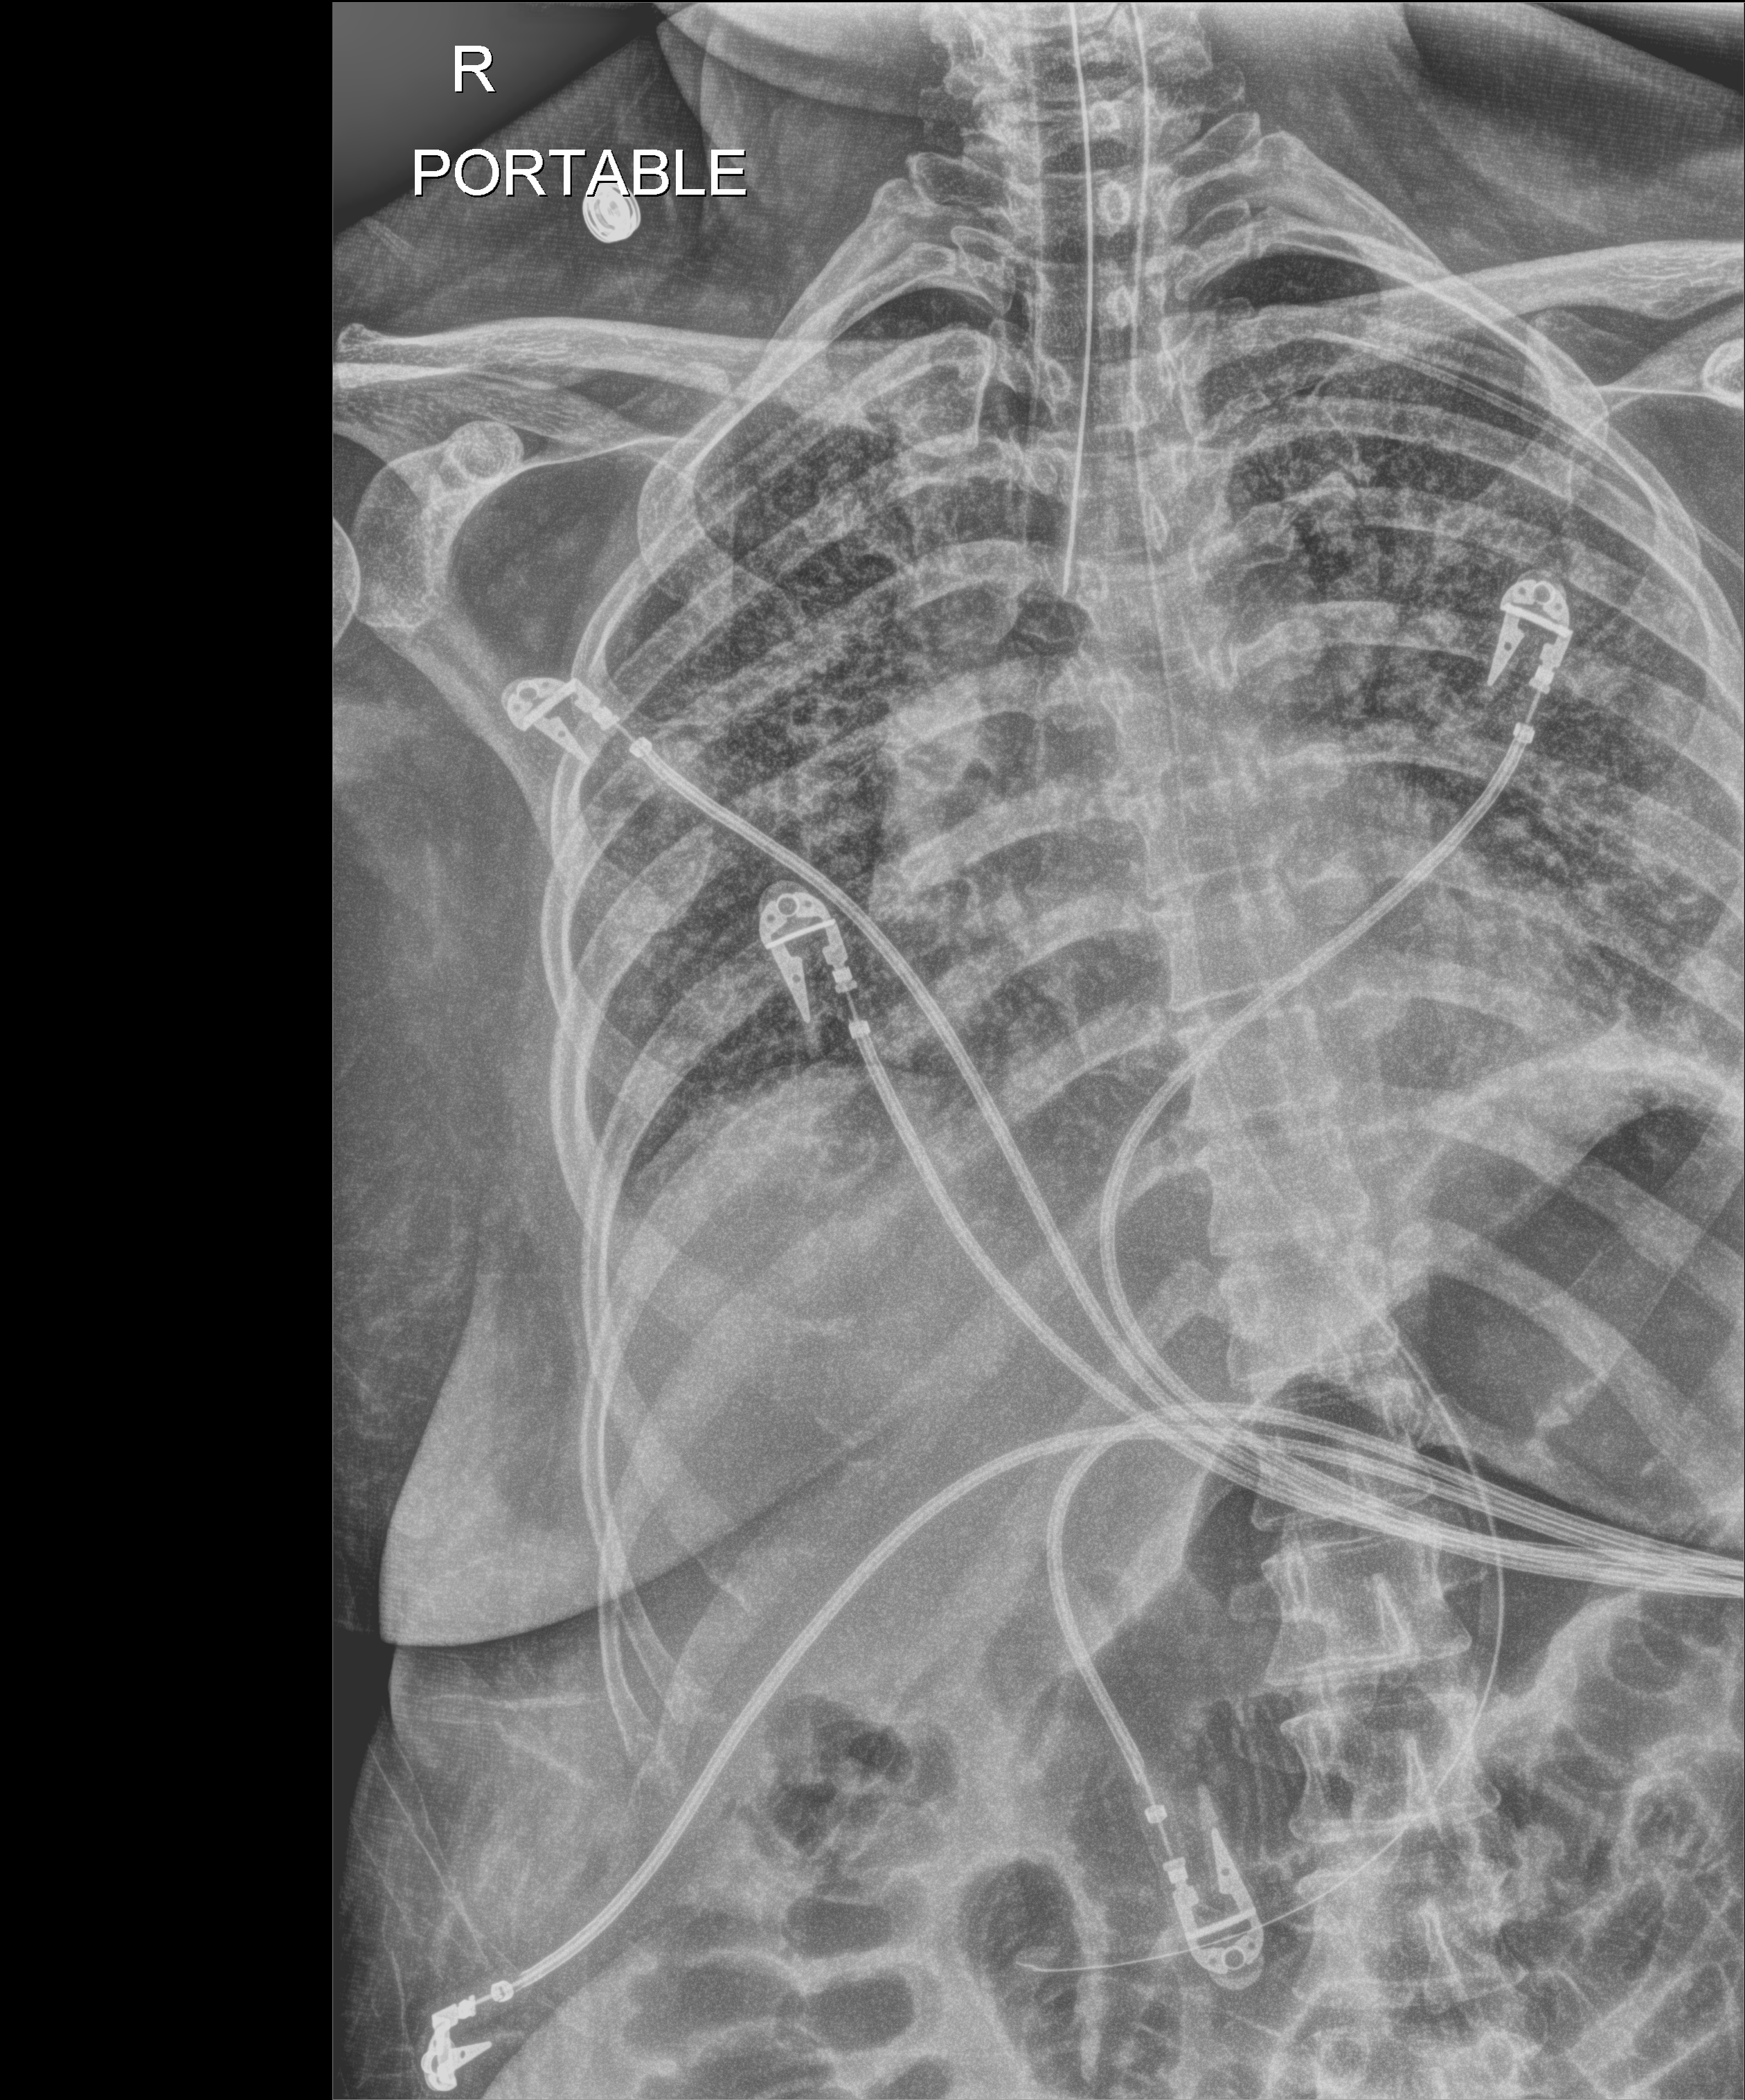
Chest X-ray (portable); anteroposterior (AP) projection. Male patient hospitalised with COVID-19, age 18–59 years.
Hospital-stay facts (about this admission, not read from this image; timing relative to this image not recorded): admitted to intensive care during this hospital stay: yes.